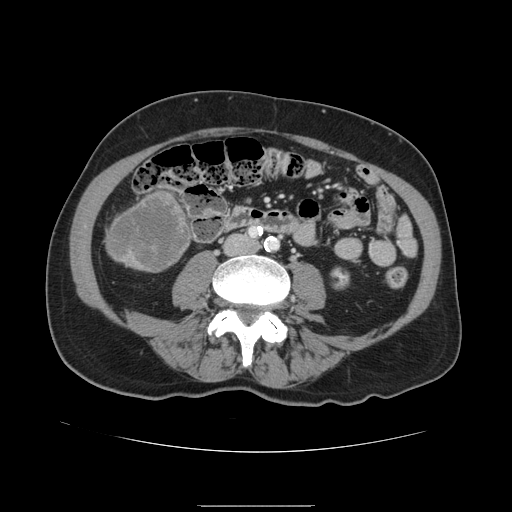
Contrast-enhanced abdominal CT, one axial slice; position 19 of 168 along the scan axis; 120 kVp; intravenous contrast given; soft-tissue window (W 400 / L 40 HU); 2.5 mm slice thickness; 512 × 512 image matrix, field of view 386 × 386 mm. Male patient, age 74 years. From the clinical record (not read from this slice): diagnosis: colorectal cancer liver metastases, imaged before liver resection; multiple liver metastases: no.
Structures marked on this image (outlined manually by an expert reader):
- liver: box from (x=106, y=188) to (x=192, y=273) px
- liver metastasis: (x=110, y=195)–(x=189, y=271)